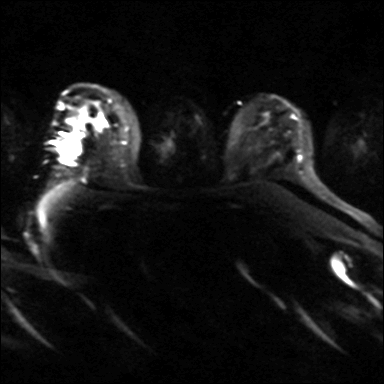
Breast MRI, one axial slice. Slice 26 of 36 in the series (ordered by position). Diffusion-weighted series; image 2 of 4 stored at this slice position (different b-values; order by instance number). 3 T. 4 mm slice thickness. 384 × 384 image matrix, field of view 320 × 320 mm. Female patient.
Structures marked on this image (outlined manually by an expert reader):
- tumour on diffusion-weighted imaging: box from (x=61, y=139) to (x=78, y=157) px